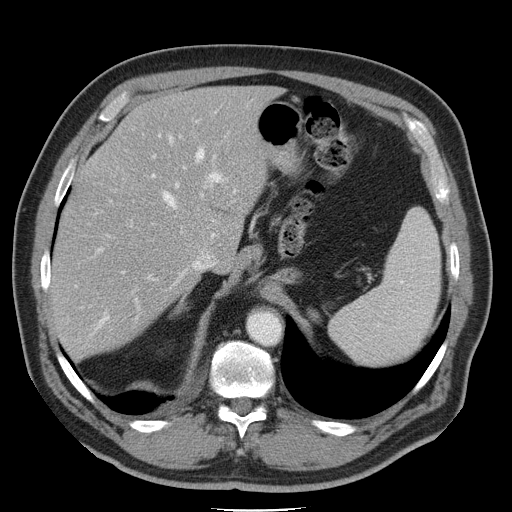
Contrast-enhanced abdominal CT, one axial slice. Intravenous contrast given. Soft-tissue window (W 400 / L 40 HU). 512 × 512 image matrix, field of view 386 × 386 mm. Male patient, age 65 years. From the clinical record (not read from this slice): diagnosis: colorectal cancer liver metastases, imaged before liver resection; multiple liver metastases: yes; largest metastasis: 4.9 cm; disease in both lobes: no.
Annotated regions visible in this slice (outlined manually by an expert reader):
- hepatic veins: bounding box <82,134,215,337> (left, top, right, bottom; pixels)
- liver: <55,87,272,356>
- planned liver remnant (the part of the liver to remain after resection): <103,87,272,260>
- portal vein (with intrahepatic branches): <96,121,221,309>